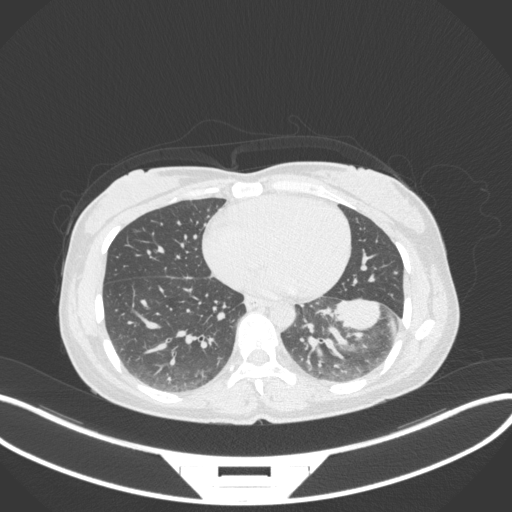
Chest CT, one axial slice; slice 139 of 361 in the series (ordered by position); reconstruction kernel B31f; lung window (W 1500 / L -600 HU); 512 × 512 image matrix, field of view 400 × 400 mm. Patient: female, 41 years. From the clinical record (not read from this slice): clinical TNM (as recorded): T2a N3 M1b.
Outlined on this slice (rectangle marked by the reading radiologist):
- lung tumour (recorded histology: adenocarcinoma): bounding box (x1, y1, x2, y2) in pixels: (332, 294, 390, 336)